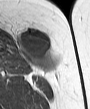
MRI of an extremity soft-tissue mass, one axial slice. Slice 22 of 45 in the series (ordered by position). MR volume resampled by the dataset authors to the PET/CT grid (not the native acquisition matrix). 90 × 109 image matrix, field of view 88 × 106 mm. Female patient. Case-level facts recorded for this patient, not image findings: histological type: leiomyosarcoma; grade: intermediate; site of the primary tumour: parascapusular.
Annotated regions visible in this slice (expert contour drawn on MRI and transferred to this co-registered scan by the dataset authors):
- gross tumour volume including surrounding oedema: bounding box <17,28,57,72> (left, top, right, bottom; pixels)
- gross tumour volume (mass): <19,30,50,65>